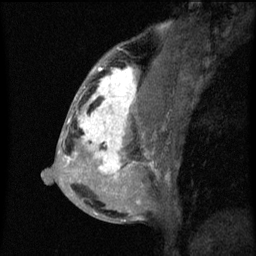
Breast MRI (dynamic contrast-enhanced), one sagittal slice; slice 28 of 60 in the series (ordered by position); dynamic contrast-enhanced series, image 2 of 3 at this slice position (ordered by acquisition); 1.5 T; TE 4.2 ms, TR 8 ms; 256 × 256 image matrix. Patient: female, 50 years.
Structures marked on this image (semi-automatically segmented with operator editing):
- analysis volume of interest (the breast-tissue region the enhancement analysis was run in; not a lesion): bounding box (x1, y1, x2, y2) in pixels: (66, 64, 141, 187)
- tumour enhancement mask (voxels above the 70 % enhancement threshold inside the analysis volume of interest): (67, 66, 137, 179)